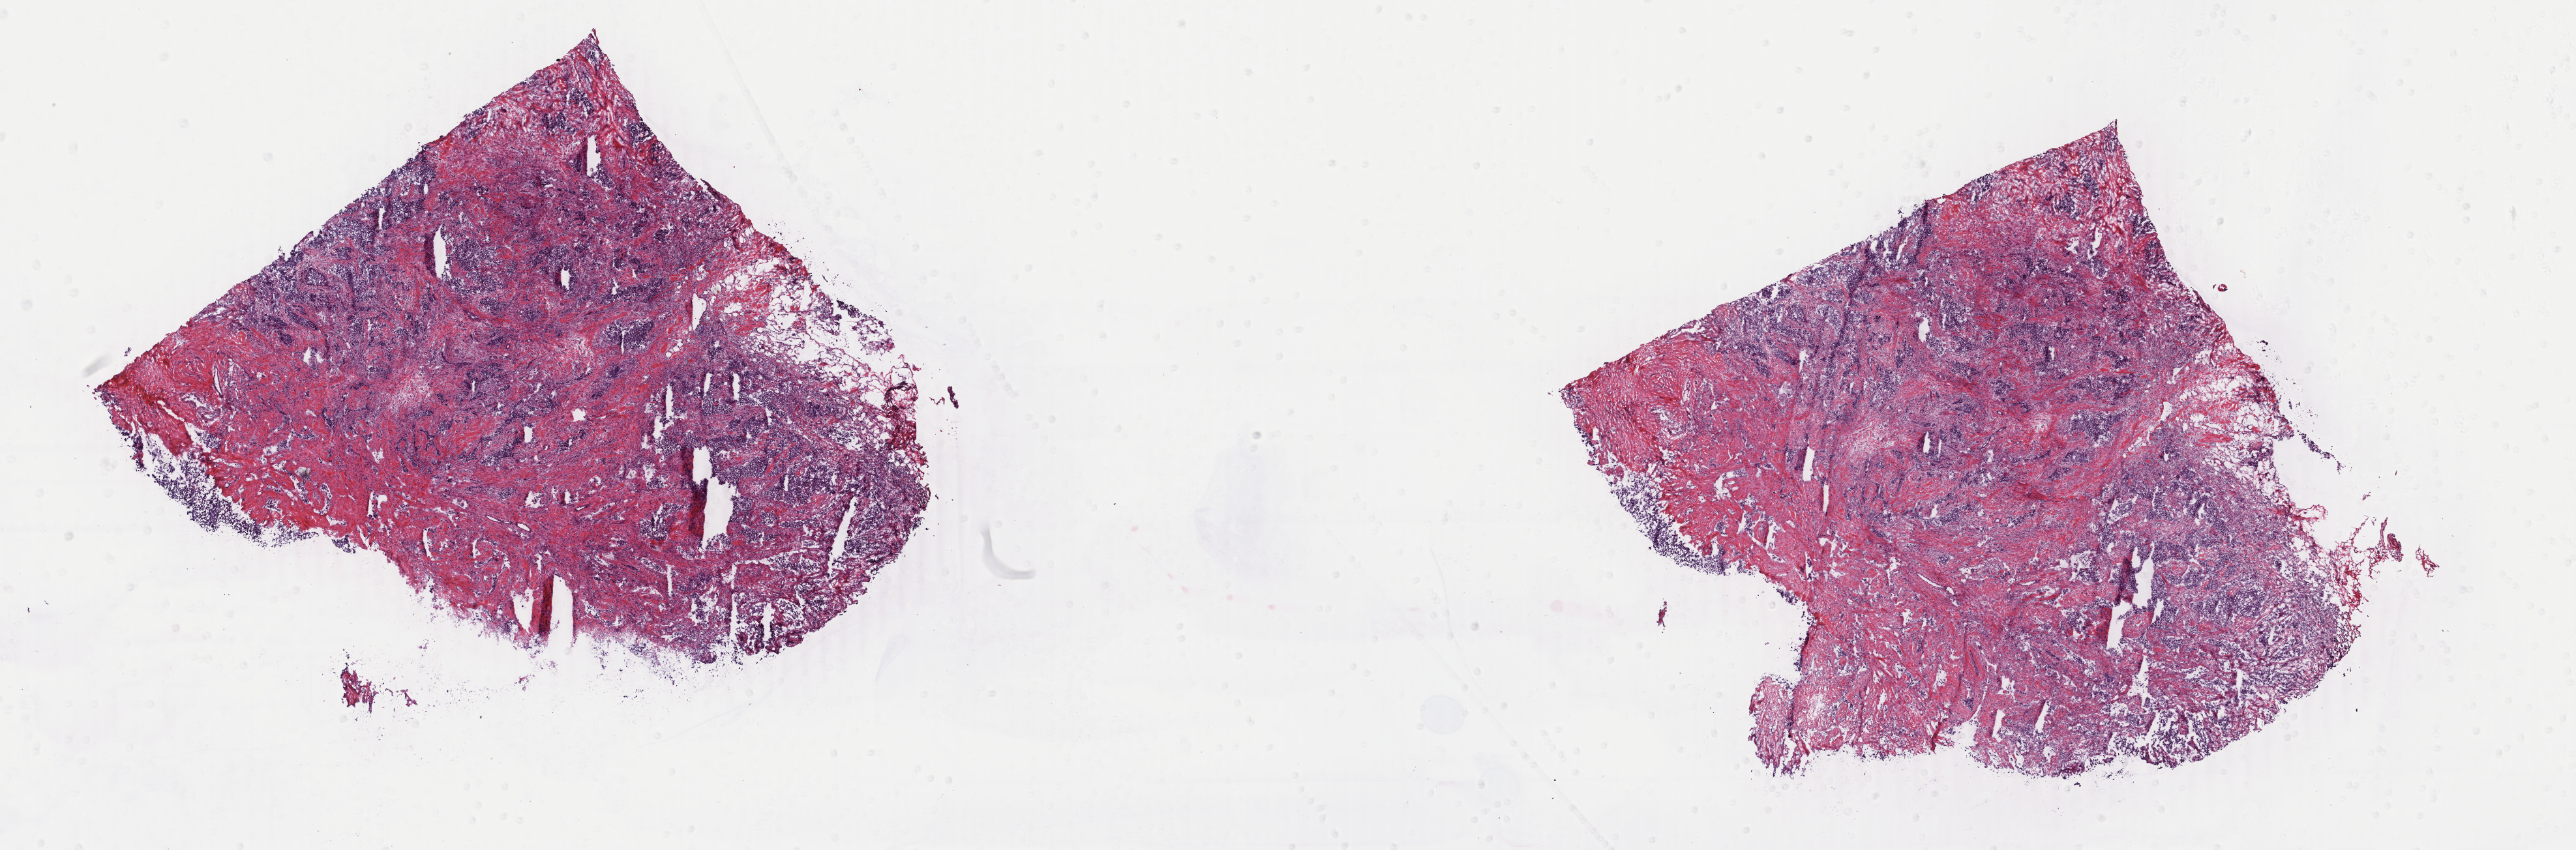
H&E whole-slide image — low-resolution overview of the scanned area, about 31.4 x 10.4 mm, frozen section from the top of the tissue portion, sample: primary tumour, breast. Female patient; age at initial diagnosis 52 years. Composition of this section per pathologist review: tumour cells 90%, tumour nuclei 60%, normal cells 0%, stromal cells 10%, necrosis 0%. Infiltration values recorded for this section: lymphocyte infiltration 0%, monocyte infiltration 0%, neutrophil infiltration 0%.
• pathologic diagnosis: Infiltrating duct carcinoma, NOS
• AJCC pathologic stage: IIA
• lymph nodes positive (case pathology): 0 of 2 examined